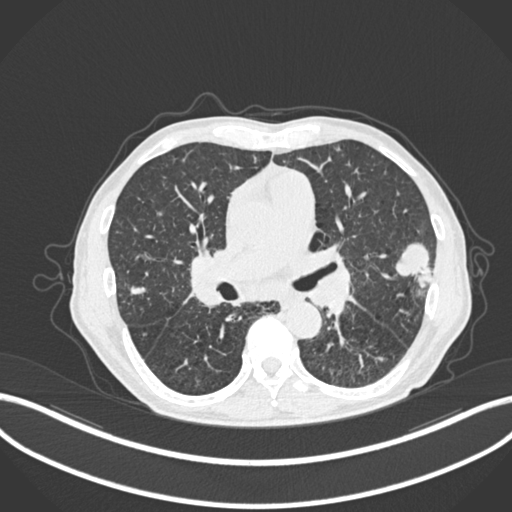
Chest CT, one axial slice. Reconstruction kernel B30f. Lung window (W 1500 / L -600 HU). 1 mm slice thickness. 512 × 512 image matrix, field of view 400 × 400 mm. Patient: male, 74 years. Case-level facts recorded for this patient, not image findings: clinical TNM (as recorded): T2a N1 M0.
Structures marked on this image (rectangle marked by the reading radiologist):
- lung tumour (recorded histology: adenocarcinoma): bounding box (x1, y1, x2, y2) in pixels: (392, 236, 436, 289)